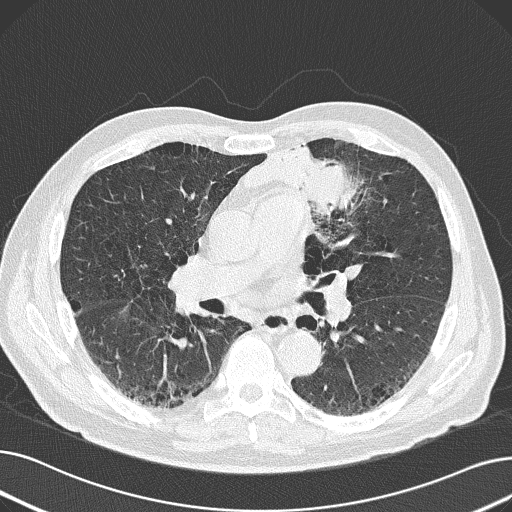
Chest CT (low-dose screening protocol), one axial image; baseline screening round; lung window (W 1500 / L -600 HU); 2 mm slice thickness; 512 × 512 image matrix. Male, age 69 years at enrolment. Former smoker at enrolment.
Expert-annotated lung lesion, box from (x=240, y=126) to (x=387, y=247) px. The exam's reader record, not a measurement of the box and not confirmed to be the same lesion: non-calcified nodule or mass ≥4 mm, left upper lobe, 6 × 10 mm, spiculated (stellate) margins, soft tissue attenuation. Later outcome: lung cancer diagnosed 20 days after this screen — non-small cell carcinoma, left upper lobe, poorly differentiated (G3), stage IB (AJCC 6th edition), 100 mm at pathology.